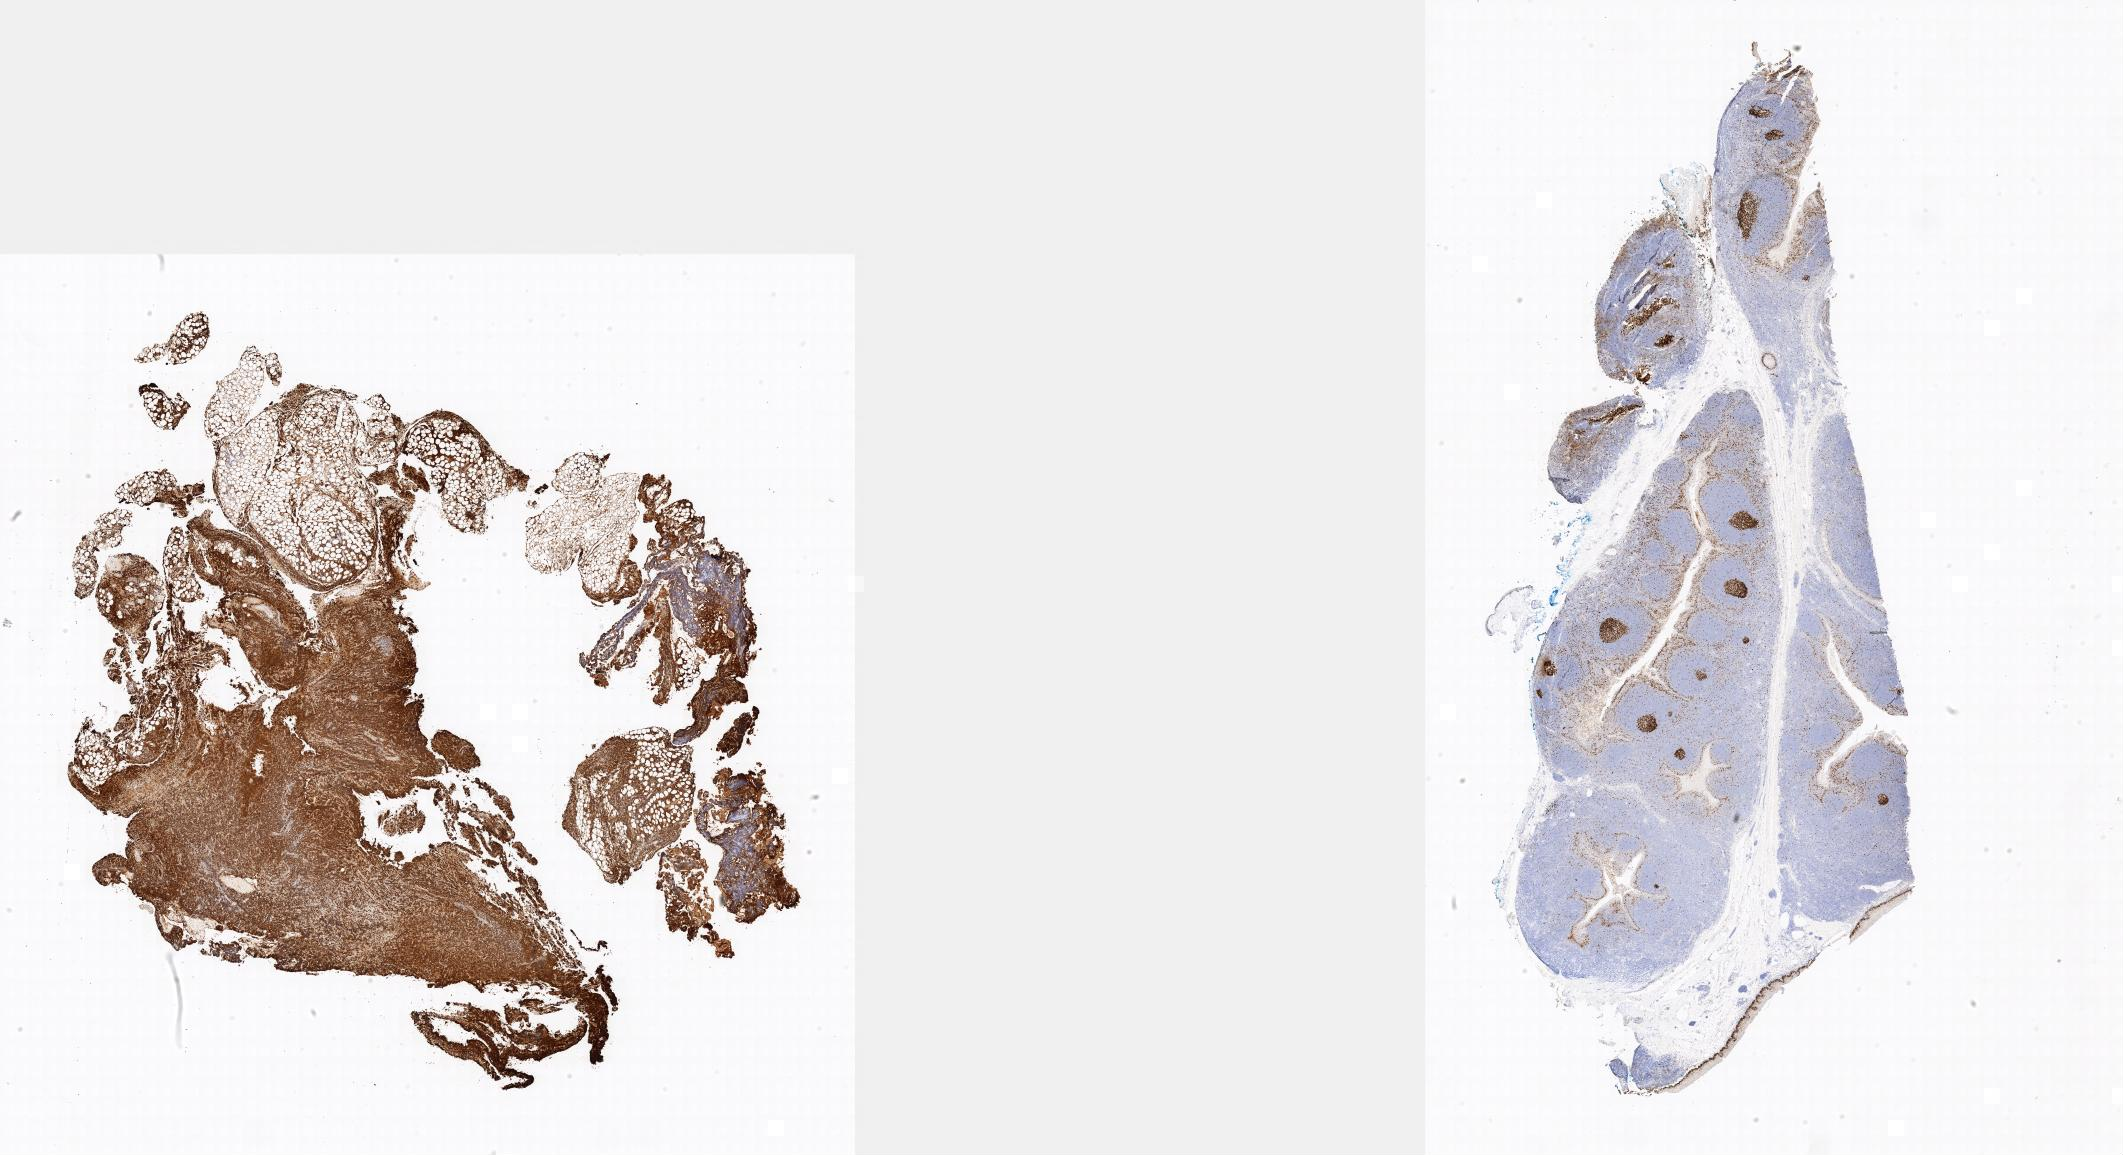
Immunohistochemistry (IHC) whole-slide image stained for Ki-67, whole scanned area shown as a low-resolution overview. Specimen: tumor tissue. Site: abdominal lymph node. Male, age 9 years at initial diagnosis.
Diagnosis: Burkitt lymphoma, NOS.